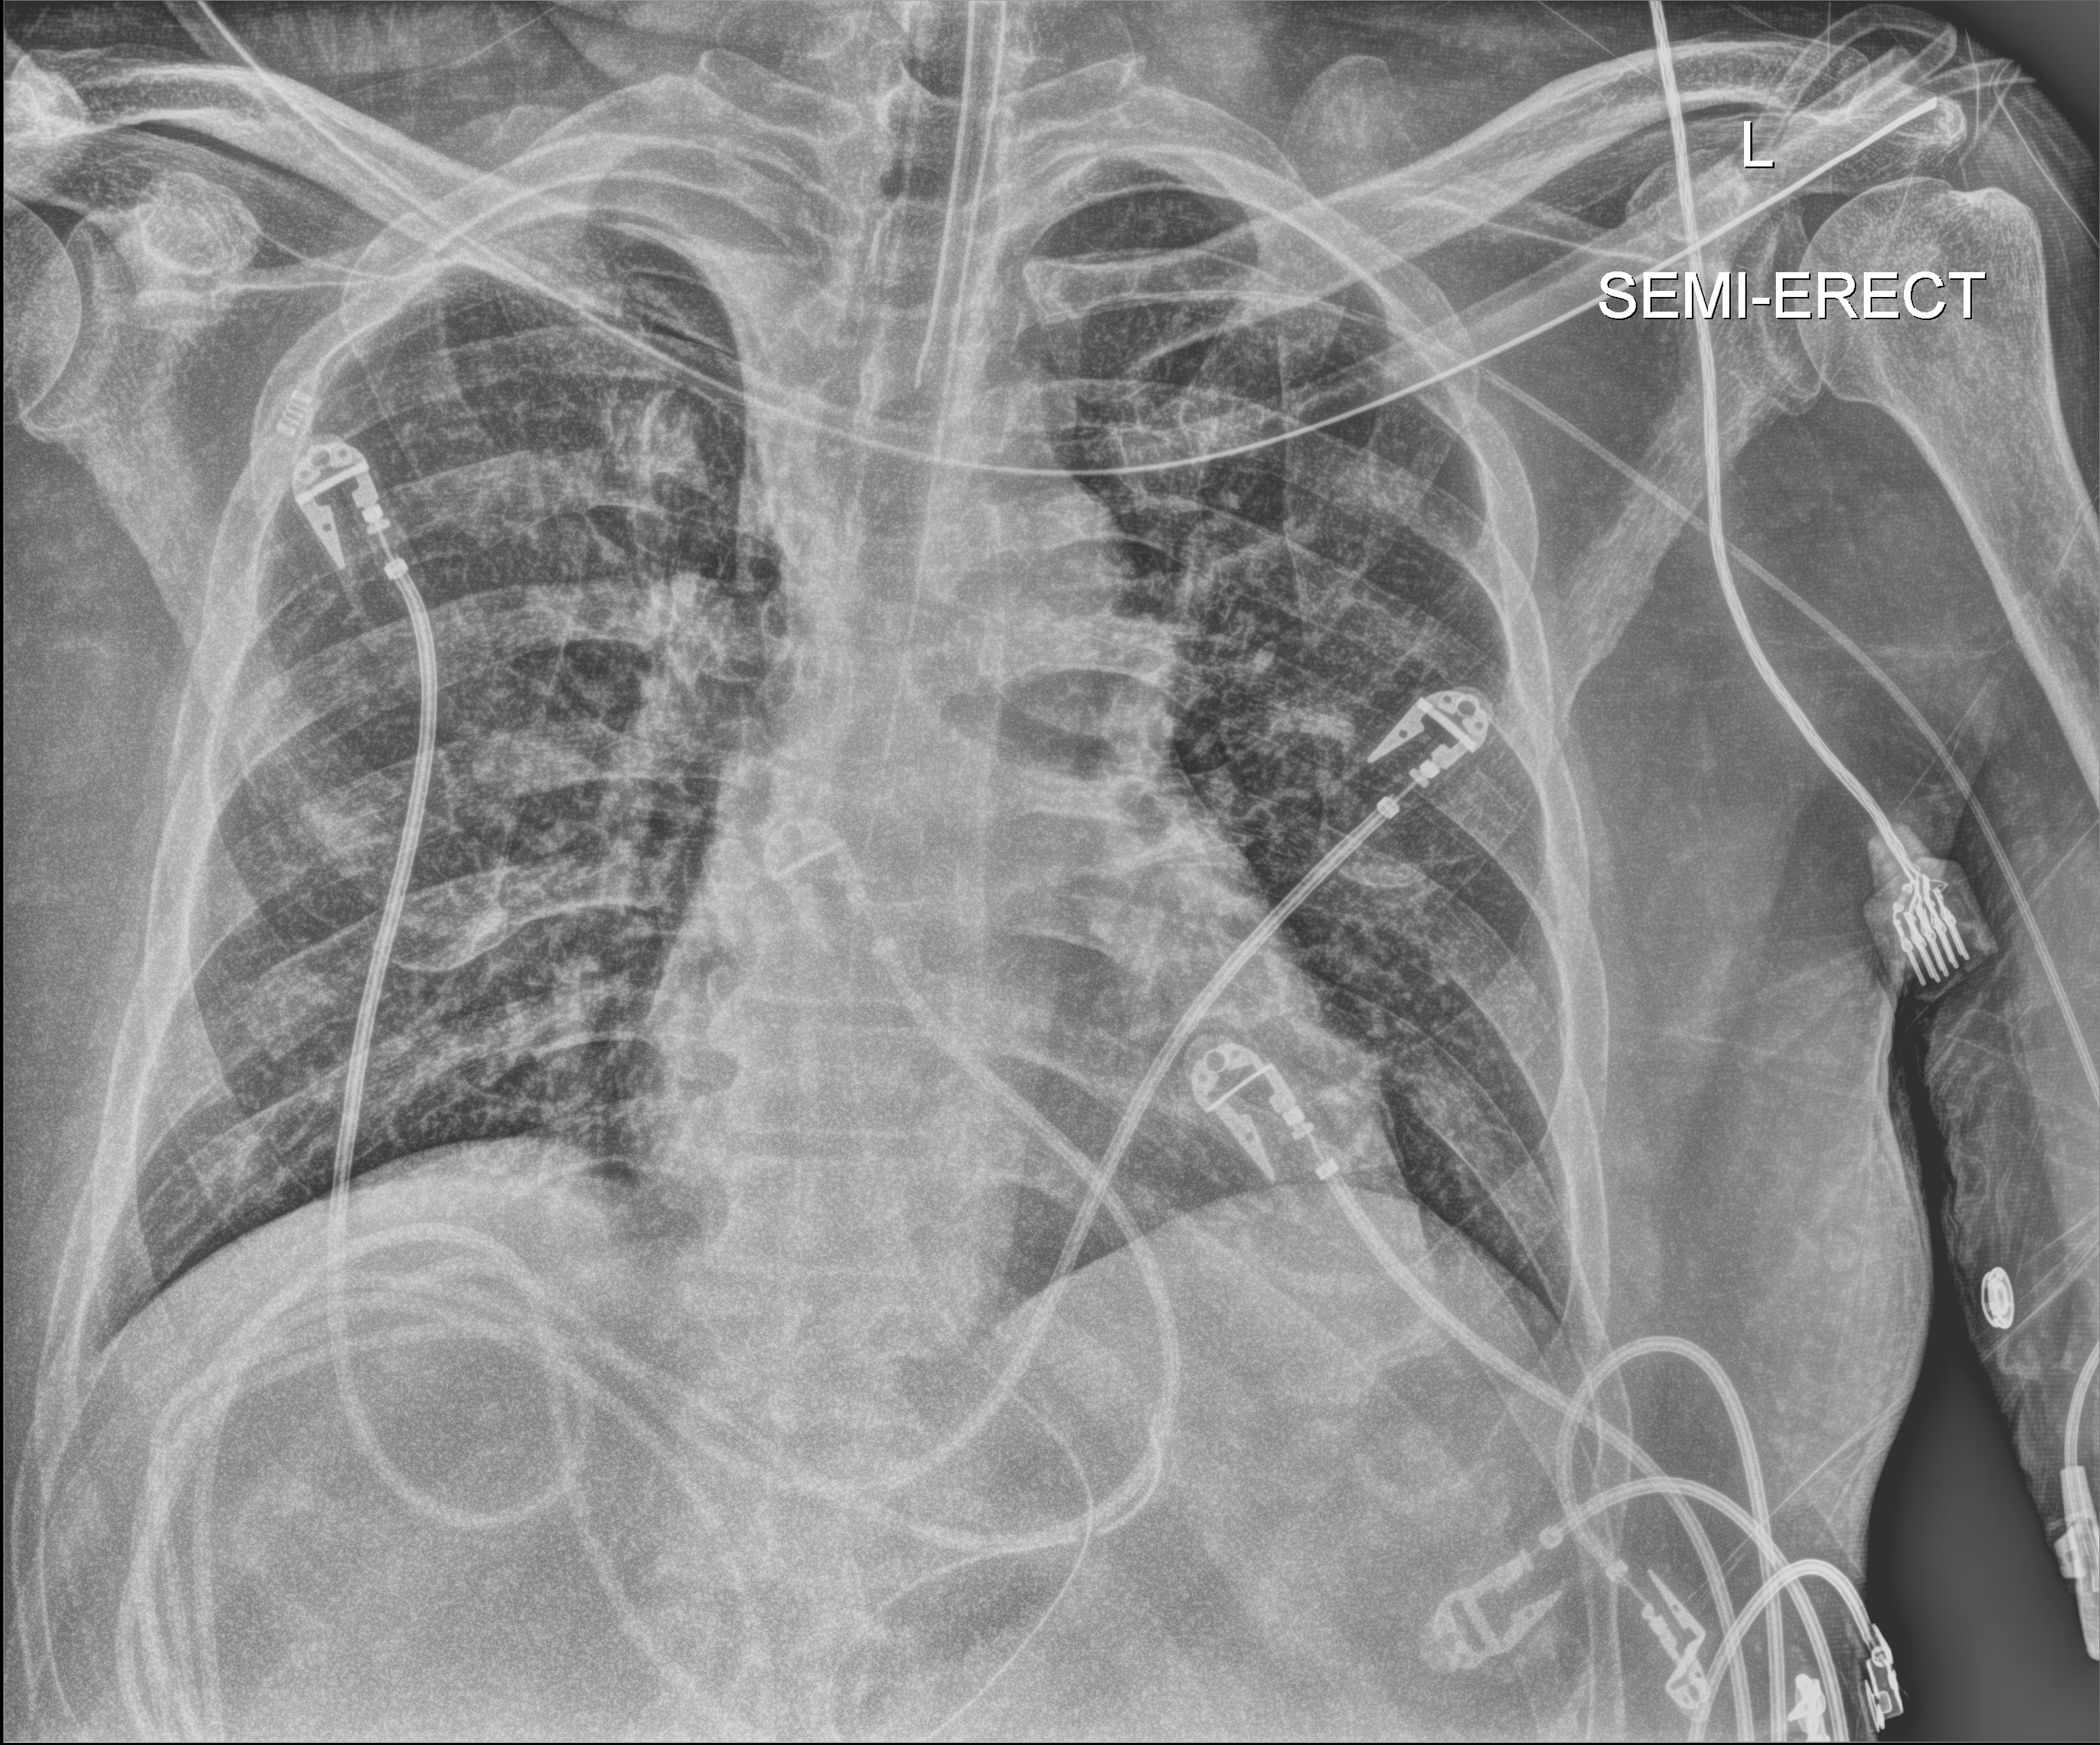
Portable chest radiograph, anteroposterior (AP) projection. Patient hospitalised with COVID-19, aged 18–59 years.
Hospital-stay facts (about this admission, not read from this image; timing relative to this image not recorded): length of hospital stay: 37 days.